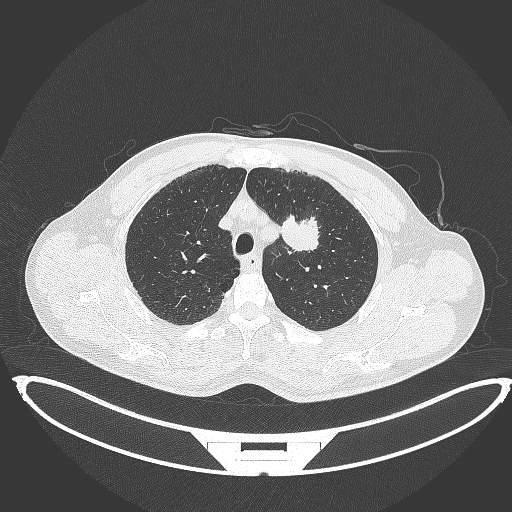
Chest CT, one axial slice. Position 345 of 395 along the scan axis. 120 kVp. Lung window (W 1500 / L -600 HU). 1 mm slice thickness. 512 × 512 image matrix. Patient: male, 60 years. From the clinical record (not read from this slice): clinical TNM (as recorded): T2a N0 M0; histopathological grade: G1-G2.
Annotated regions visible in this slice (rectangle marked by the reading radiologist):
- lung tumour (recorded histology: squamous cell carcinoma): bounding box <279,211,320,256> (left, top, right, bottom; pixels)